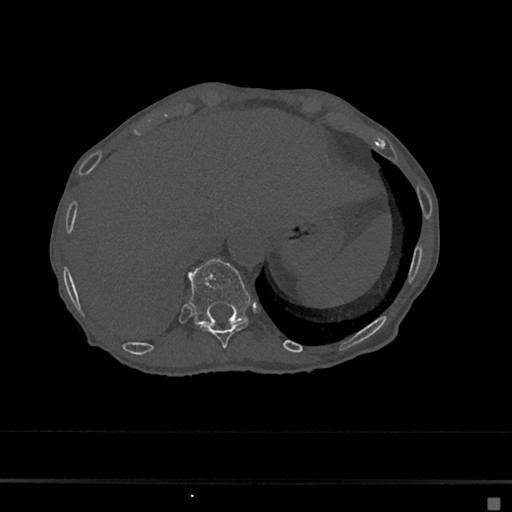
CT including the spine, one axial slice. Slice 197 of 797 in the series (ordered by position). Reconstruction kernel Br40s/3. 120 kVp. Bone window (W 1800 / L 400 HU). 0.5 mm slice thickness. 512 × 512 image matrix, field of view 360 × 360 mm. Female patient, age 68 years. From the clinical record (not read from this slice): primary cancer: renal.
Structures marked on this image (semi-automatically segmented with operator editing):
- T10 vertebra: bounding box <197,321,248,348> (left, top, right, bottom; pixels)
- T11 vertebra: <188,259,251,325>